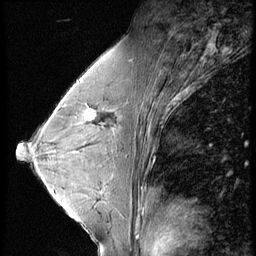
Breast MRI (dynamic contrast-enhanced), one sagittal slice; position 36 of 56 along the scan axis; 4 images stored at this slice position (order not interpretable as contrast timing); 1.5 T; TE 4.2 ms, TR 9 ms; 256 × 256 image matrix. Female patient, age 45 years. Case-level facts recorded for this patient, not image findings: setting: breast cancer imaged before/during neoadjuvant chemotherapy; receptor status: triple-negative.
Annotated regions visible in this slice (semi-automatic segmentation, software-assisted and operator-edited):
- analysis volume of interest (the breast-tissue region the enhancement analysis was run in; not a lesion): bounding box [x1, y1, x2, y2] px = [77, 104, 97, 124]
- tumour enhancement mask (voxels above the 140 % enhancement threshold inside the analysis volume of interest): [77, 109, 94, 124]